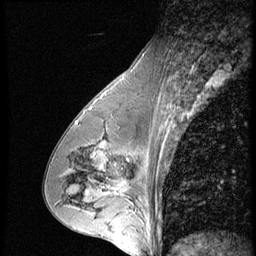
Breast MRI (dynamic contrast-enhanced), one sagittal slice; slice 29 of 56 in the series (ordered by position); 3 images stored at this slice position (order not interpretable as contrast timing); 1.5 T; TE 4.2 ms, TR 9 ms; 256 × 256 image matrix. Patient: female, 43 years. From the clinical record (not read from this slice): setting: breast cancer imaged before/during neoadjuvant chemotherapy; receptor status: HR-positive, HER2-negative.
Structures marked on this image (semi-automatically segmented with operator editing):
- analysis volume of interest (the breast-tissue region the enhancement analysis was run in; not a lesion): box from (x=120, y=160) to (x=163, y=207) px
- tumour enhancement mask (voxels above the 140 % enhancement threshold inside the analysis volume of interest): (x=126, y=202)–(x=129, y=205)